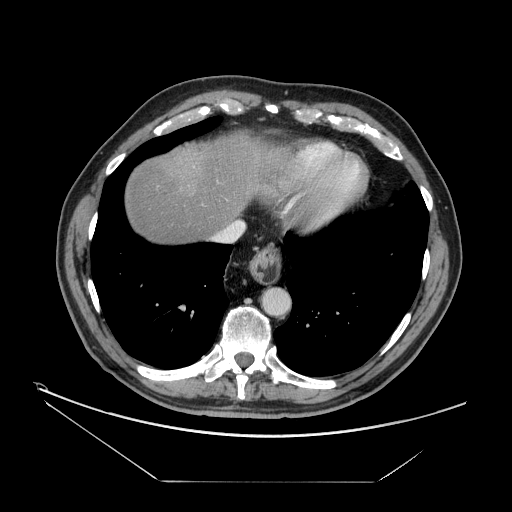
Contrast-enhanced abdominal CT, one axial slice. Position 145 of 161 along the scan axis. Reconstruction kernel STANDARD. 120 kVp. Intravenous contrast given. Soft-tissue window (W 400 / L 40 HU). 2.5 mm slice thickness. 512 × 512 image matrix. Male patient, age 65 years. Case-level facts recorded for this patient, not image findings: diagnosis: colorectal cancer liver metastases, imaged before liver resection.
Outlined on this slice (outlined manually by an expert reader):
- hepatic veins: bounding box (x1, y1, x2, y2) in pixels: (216, 221, 245, 242)
- liver: (124, 134, 265, 244)
- planned liver remnant (the part of the liver to remain after resection): (125, 133, 266, 243)